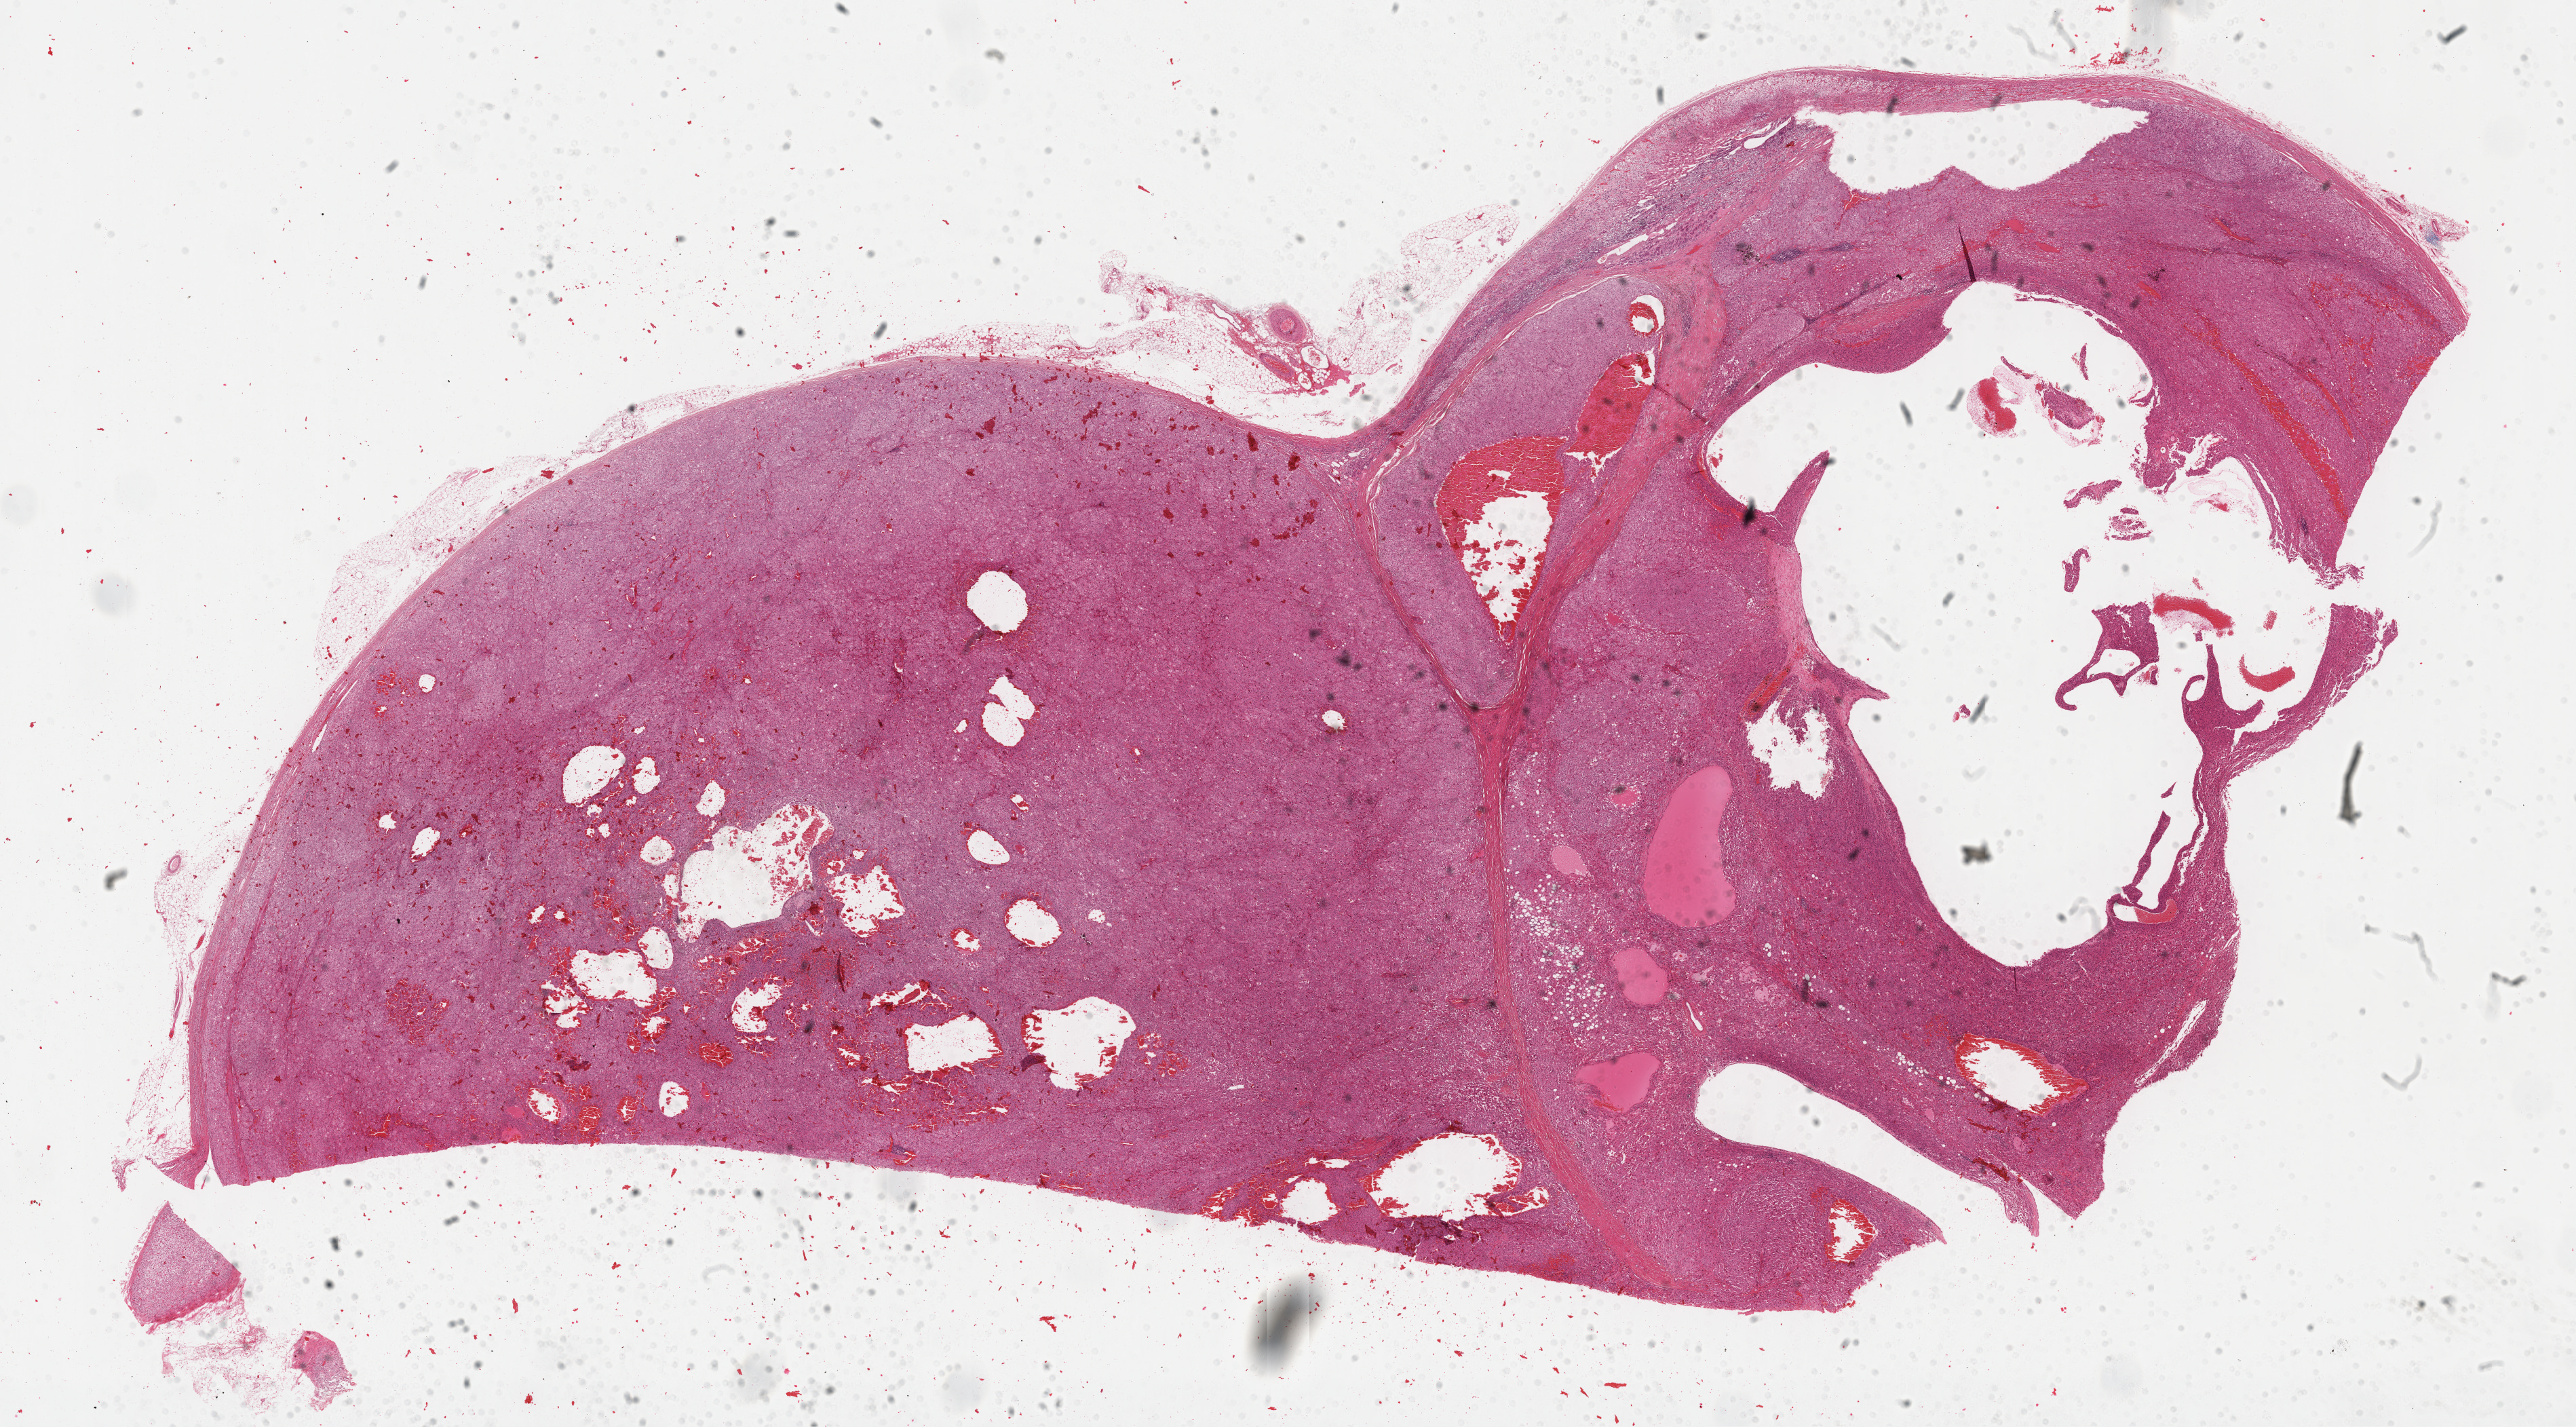
H&E-stained whole-slide image — shown as a low-resolution overview of the whole scanned area (about 30.7 x 17.0 mm); formalin-fixed paraffin-embedded (FFPE) diagnostic section; primary tumour sample from the adrenal cortex. Patient: male, age at initial diagnosis 22 years.
• histologic diagnosis: Adrenal cortical carcinoma